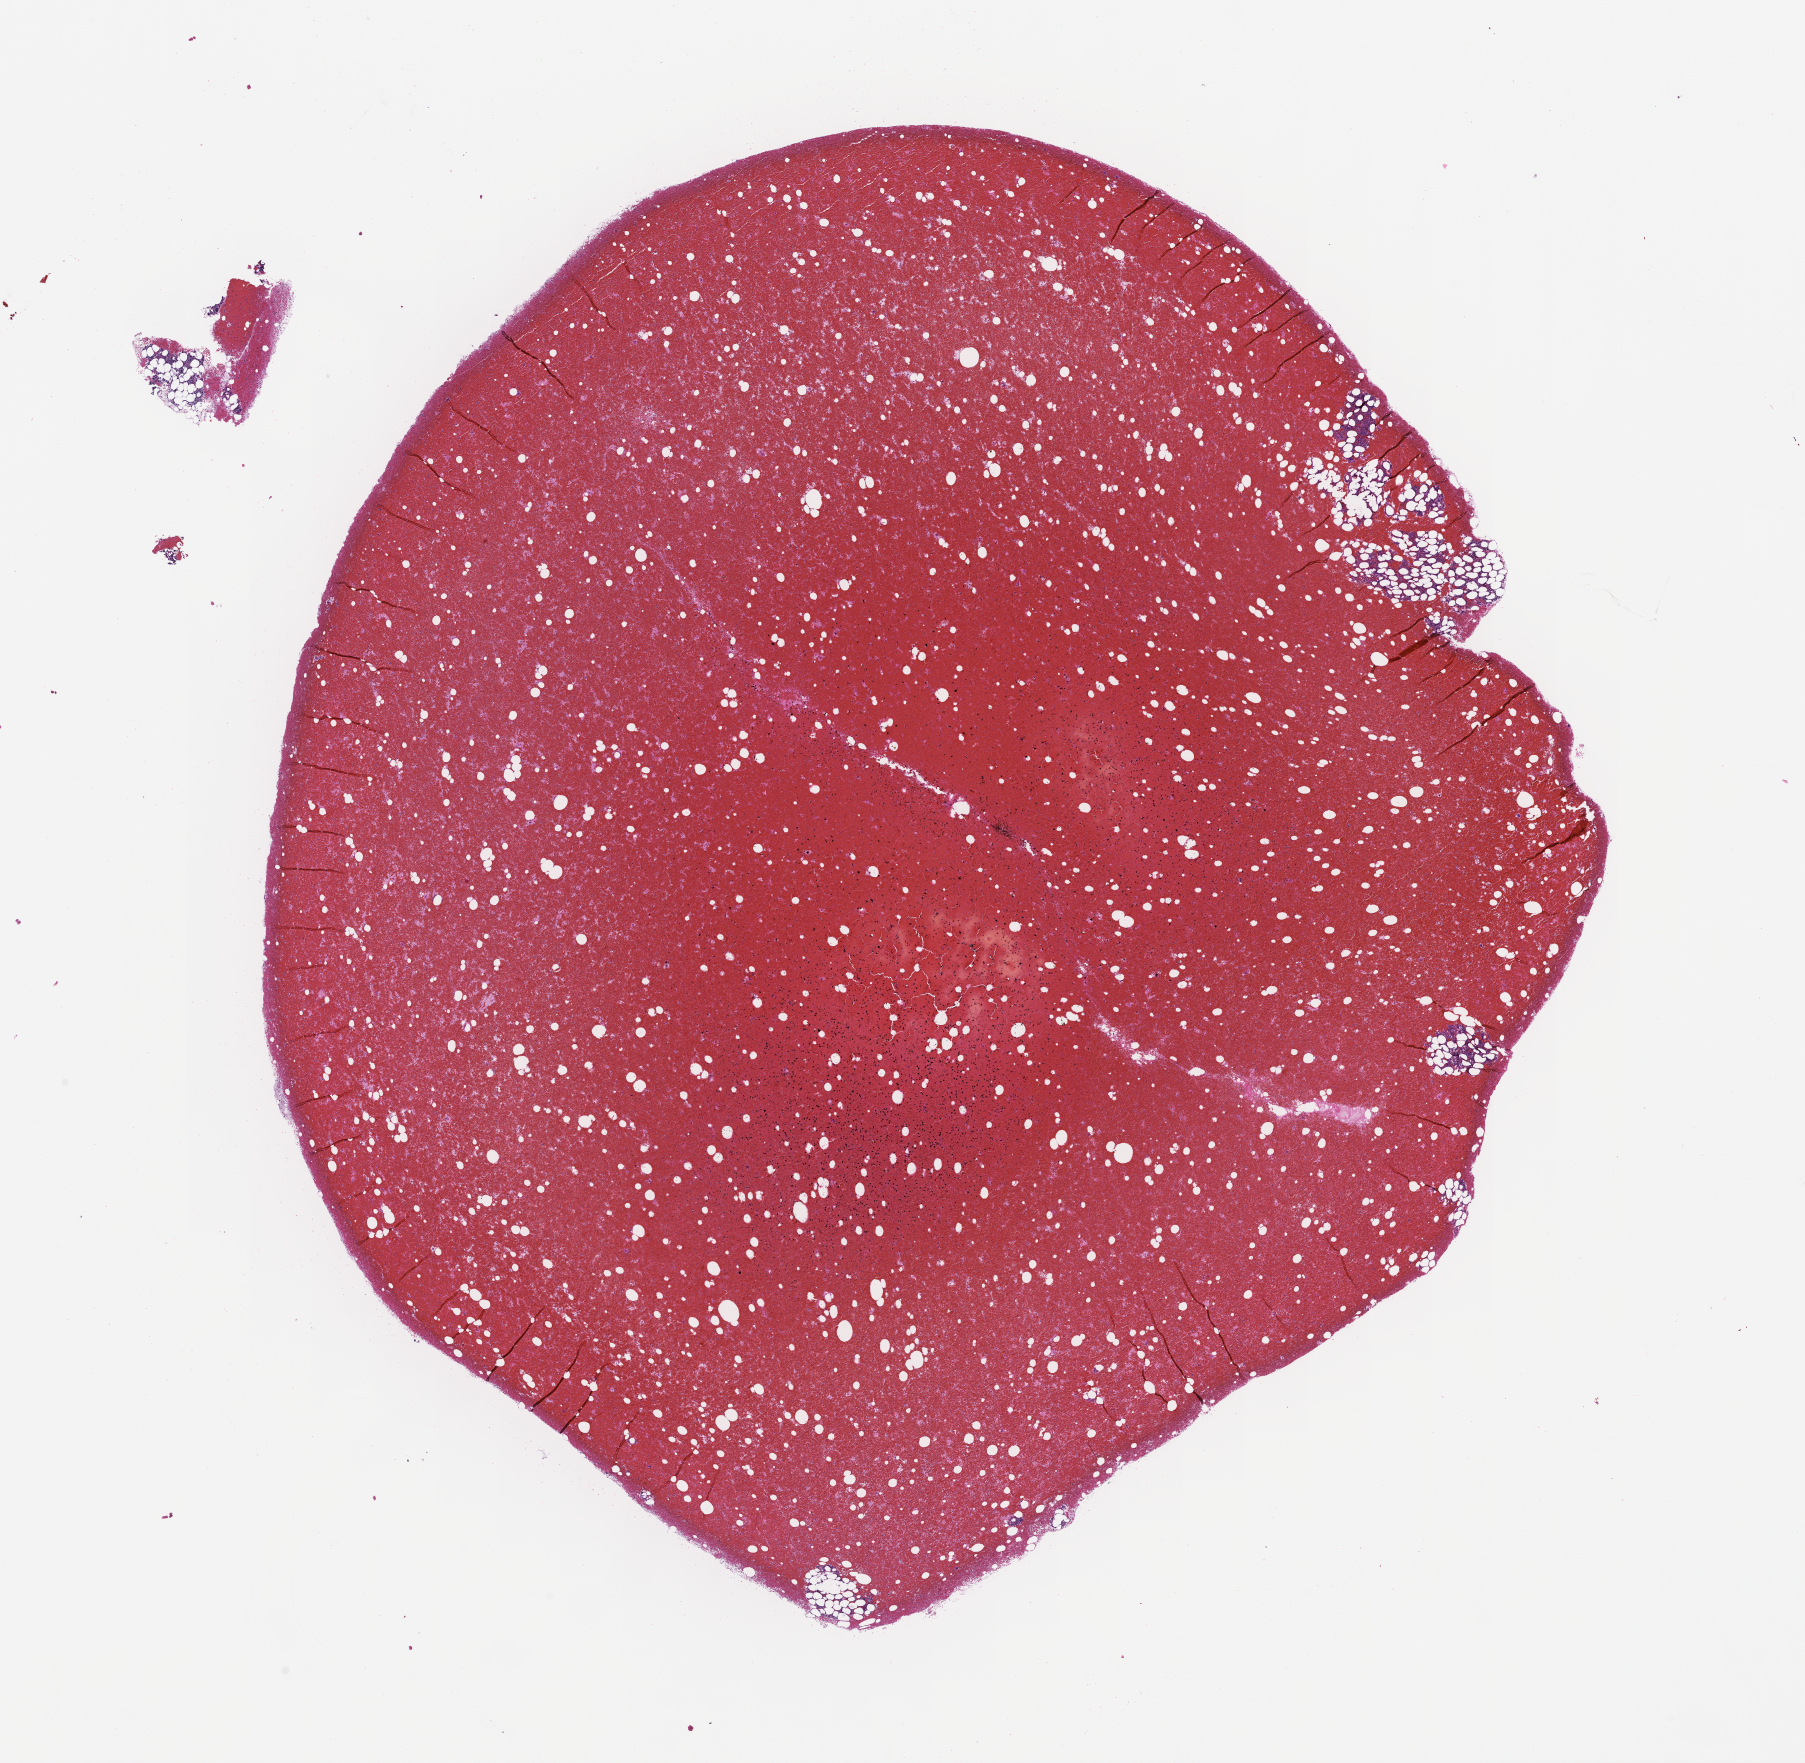
Digitized hematoxylin and eosin (H&E)-stained section — shown as a low-resolution overview of the whole scanned area (about 14.6 x 14.2 mm); formalin-fixed paraffin-embedded section; site: bone marrow. Patient: male.
This section: primary tumour tissue. Diagnosis: Plasma Cell Myeloma.